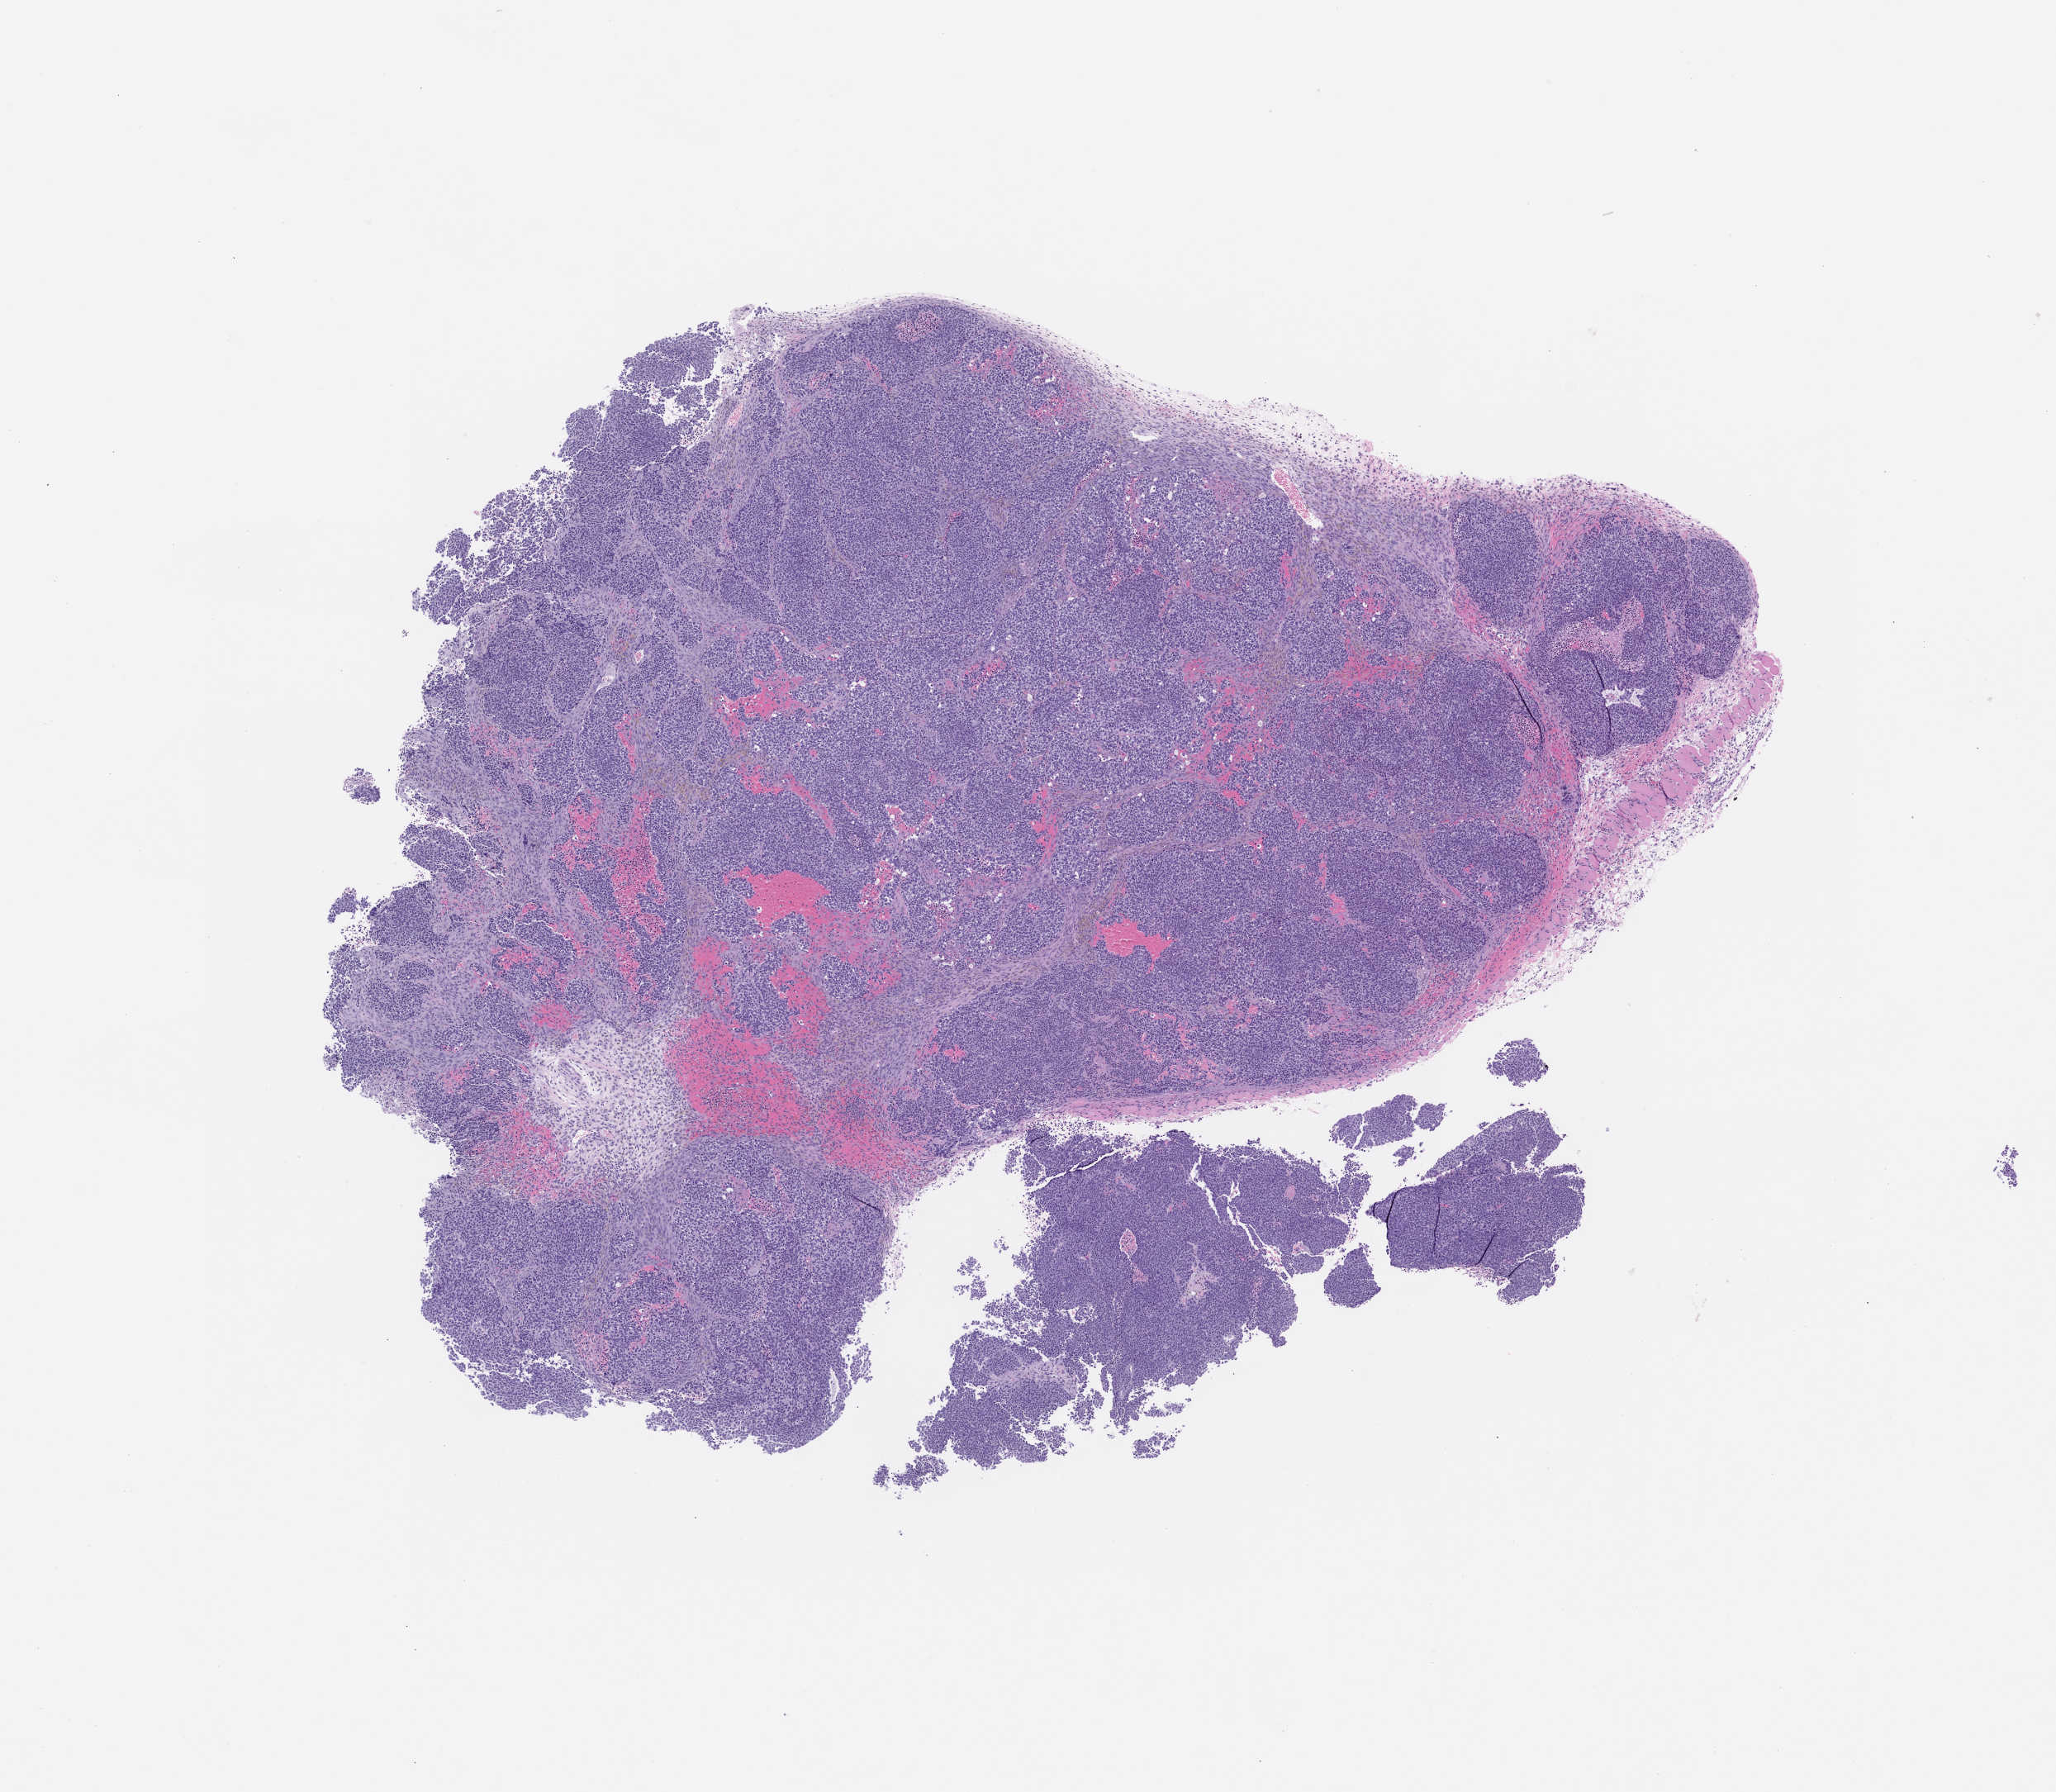
H&E whole-slide image of a patient-derived xenograft (PDX) tumor grown in a mouse, whole scanned area (about 10.0 x 8.7 mm) shown as a low-resolution overview, FFPE section, originating tumor site category: lung.
Originating patient diagnosis: Lung Adenocarcinoma.